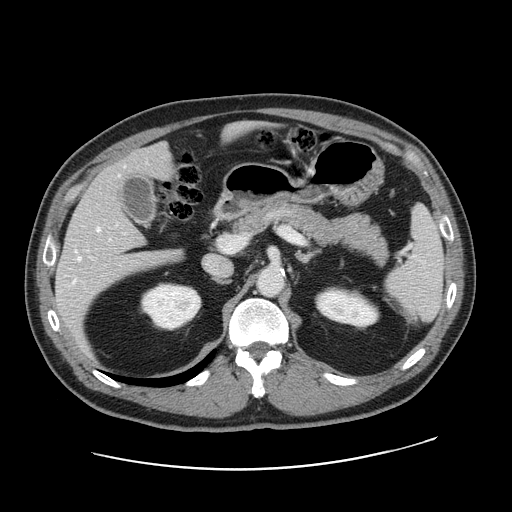
Contrast-enhanced abdominal CT, one axial slice. Intravenous contrast given. Soft-tissue window (W 400 / L 40 HU). 512 × 512 image matrix, field of view 403 × 403 mm. Male patient, age 63 years. From the clinical record (not read from this slice): diagnosis: colorectal cancer liver metastases, imaged before liver resection; multiple liver metastases: yes; largest metastasis: 8 cm; chemotherapy before resection: no.
Outlined on this slice (manually delineated by an expert):
- hepatic veins: bounding box <73,227,100,282> (left, top, right, bottom; pixels)
- liver: <56,125,251,341>
- planned liver remnant (the part of the liver to remain after resection): <117,125,251,180>
- portal vein (with intrahepatic branches): <92,236,247,258>